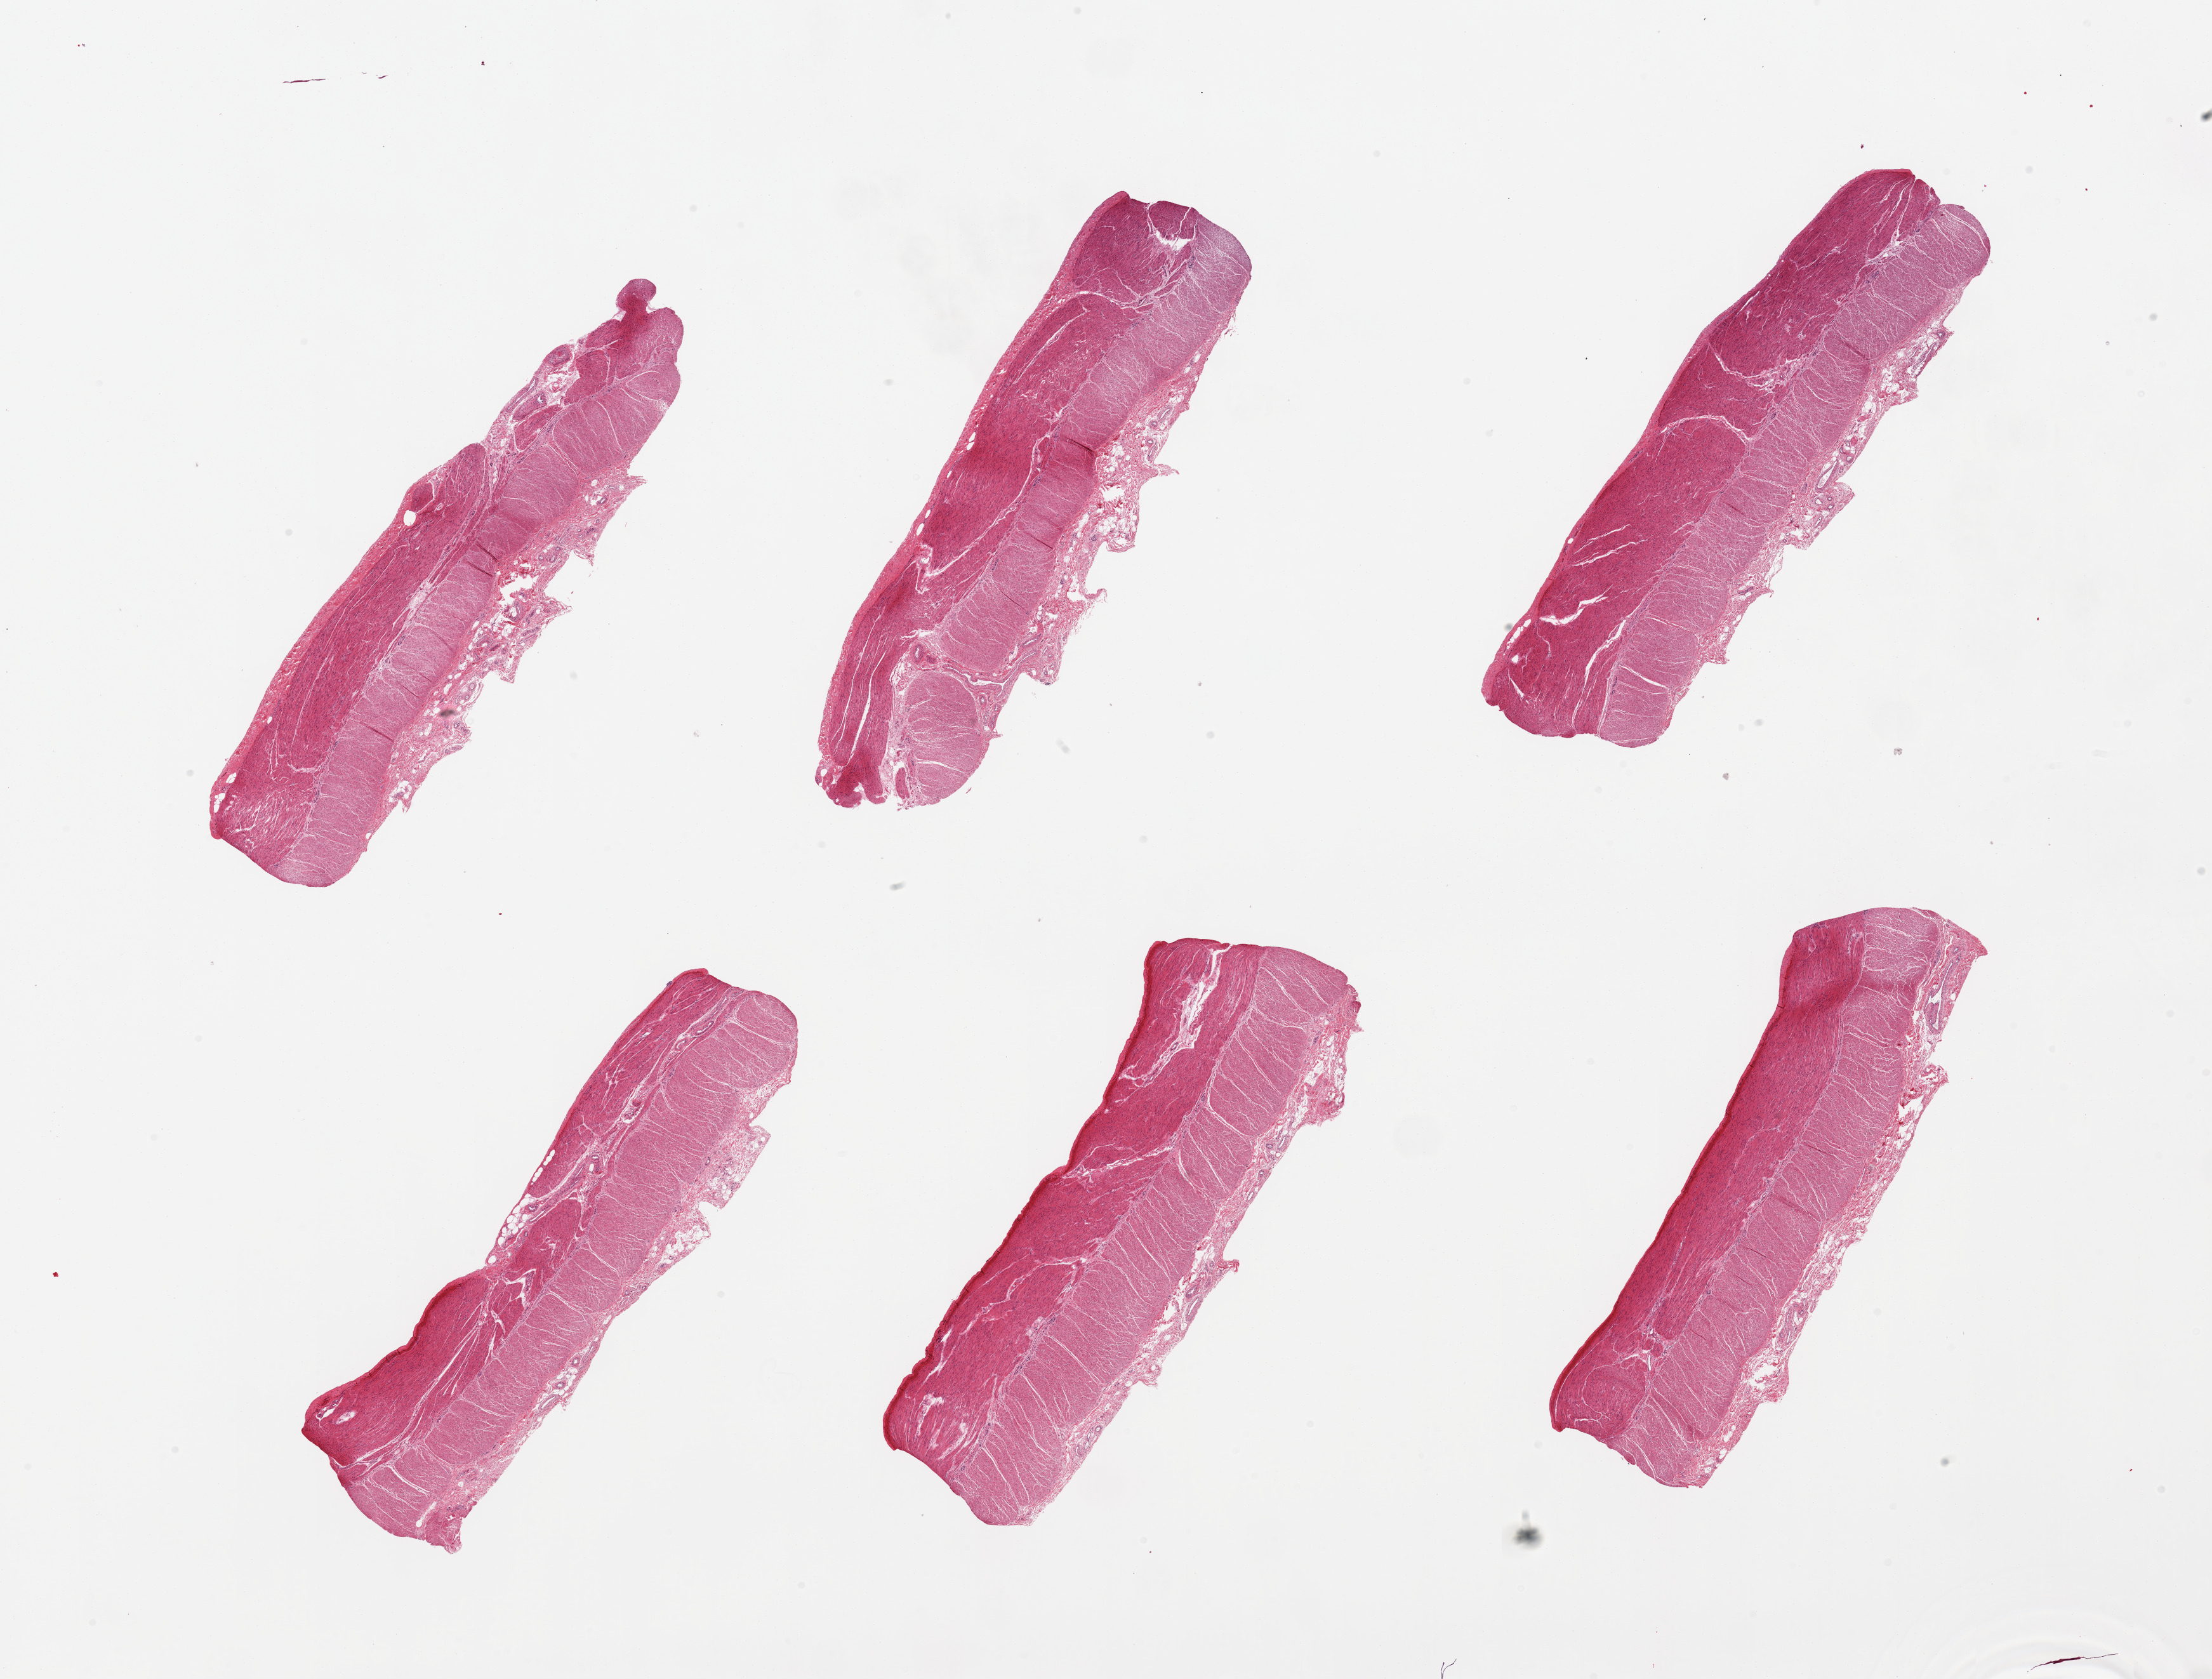
Digitized hematoxylin and eosin (H&E)-stained section, brightfield, low-resolution overview of the scanned area, about 27.6 x 20.9 mm, PAXgene-fixed, paraffin-embedded tissue, sampled site (target tissue): sigmoid colon, donor tissue sample. Donor: male.
- review note (as recorded): 2 pieces, all target muscularis